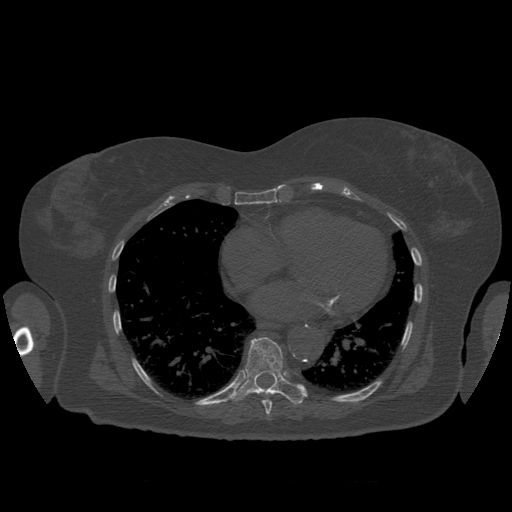
CT including the spine, one axial slice; position 365 of 399 along the scan axis; 120 kVp; bone window (W 1800 / L 400 HU); 1.25 mm slice thickness; 512 × 512 image matrix, field of view 404 × 404 mm. Patient age 81 years. Case-level facts recorded for this patient, not image findings: primary cancer: renal.
Annotated regions visible in this slice (semi-automatic segmentation, software-assisted and operator-edited):
- T8 vertebra: box from (x=262, y=395) to (x=272, y=416) px
- T9 vertebra: (x=231, y=337)–(x=304, y=405)